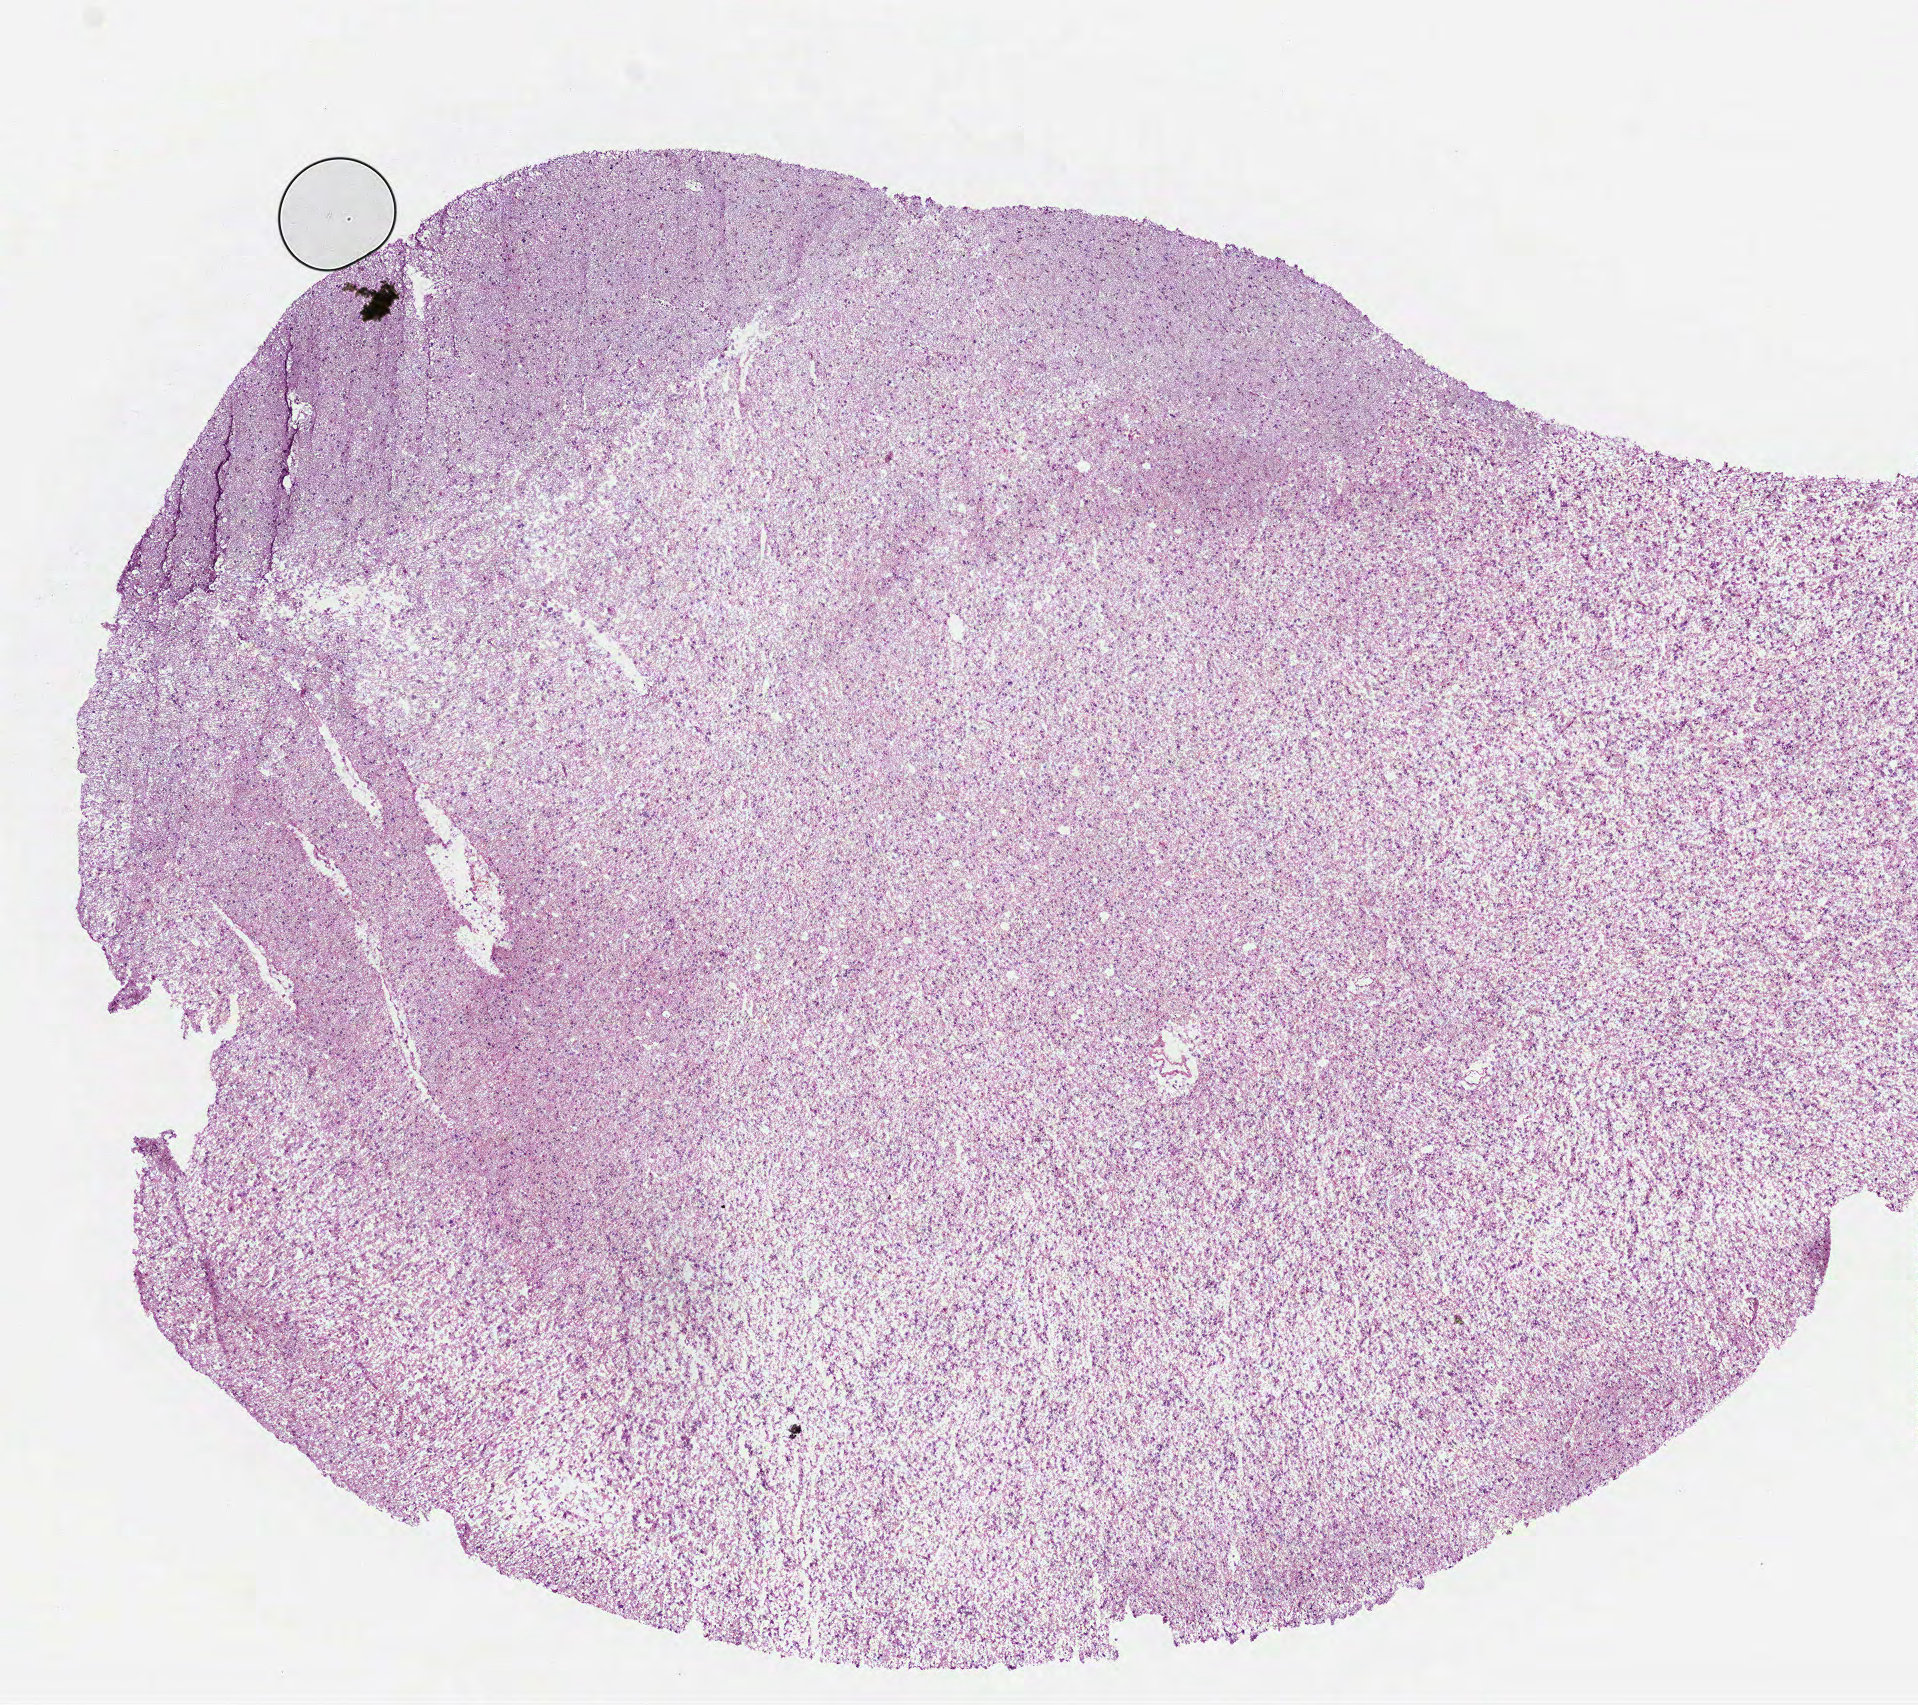
Whole-slide histology image, H&E, shown as a low-resolution overview of the whole scanned area (about 7.7 x 6.9 mm); frozen section from the bottom of the tissue portion; sample: primary tumour, brain. Female patient; age at initial diagnosis 38 years. Histologic grade: G3 (poorly differentiated). Composition of this section per pathologist review: tumour cells 100%, tumour nuclei 70%, normal cells 0%, stromal cells 0%, necrosis 0%.
Diagnosis: Astrocytoma, anaplastic.